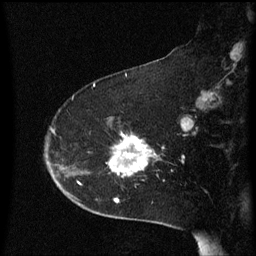
Breast MRI (dynamic contrast-enhanced), one sagittal slice. Dynamic contrast-enhanced series, image 2 of 3 at this slice position (ordered by acquisition). 1.5 T. TE 4.2 ms, TR 8.4 ms. 2 mm slice thickness. 256 × 256 image matrix, field of view 200 × 200 mm. Female patient, age 54 years. Case-level facts recorded for this patient, not image findings: setting: breast cancer imaged before/during neoadjuvant chemotherapy; receptor status: HR-positive, HER2-negative.
Structures marked on this image (semi-automatically segmented with operator editing):
- analysis volume of interest (the breast-tissue region the enhancement analysis was run in; not a lesion): bounding box <101,120,165,177> (left, top, right, bottom; pixels)
- tumour enhancement mask (voxels above the 70 % enhancement threshold inside the analysis volume of interest): <110,136,157,177>